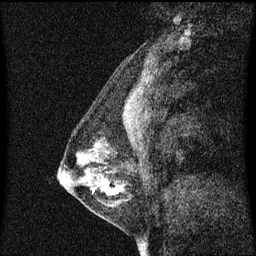
Breast MRI (dynamic contrast-enhanced), one sagittal slice; slice 21 of 60 in the series (ordered by position); dynamic contrast-enhanced series, image 2 of 3 at this slice position (ordered by acquisition); 1.5 T; TE 4.2 ms, TR 8.4 ms; 2 mm slice thickness; 256 × 256 image matrix. Female patient, age 41 years. Case-level facts recorded for this patient, not image findings: setting: breast cancer imaged before/during neoadjuvant chemotherapy; receptor status: triple-negative.
Annotated regions visible in this slice (semi-automatic segmentation, software-assisted and operator-edited):
- analysis volume of interest (the breast-tissue region the enhancement analysis was run in; not a lesion): bounding box <64,138,131,209> (left, top, right, bottom; pixels)
- tumour enhancement mask (voxels above the 70 % enhancement threshold inside the analysis volume of interest): <106,188,117,195>